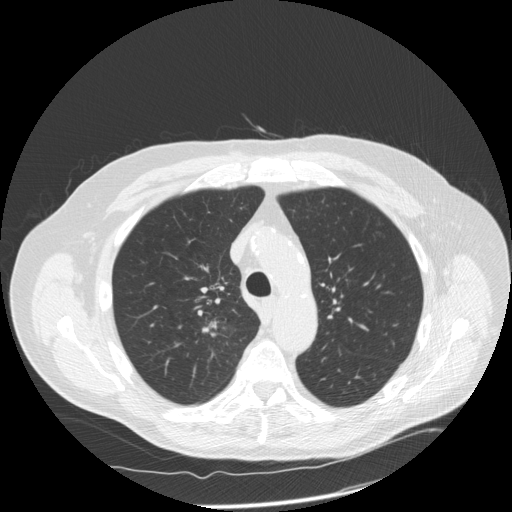
Low-dose screening chest CT, one axial slice; slice 120 of 166 in the series (ordered by position); reconstruction kernel STANDARD; lung window (W 1500 / L -600 HU); 2.5 mm slice thickness; 512 × 512 image matrix.
Annotated regions visible in this slice (outlined manually by an expert reader):
- lesion 1 (tumor, upper lobe of right lung): bounding box [x1, y1, x2, y2] px = [203, 322, 218, 333]